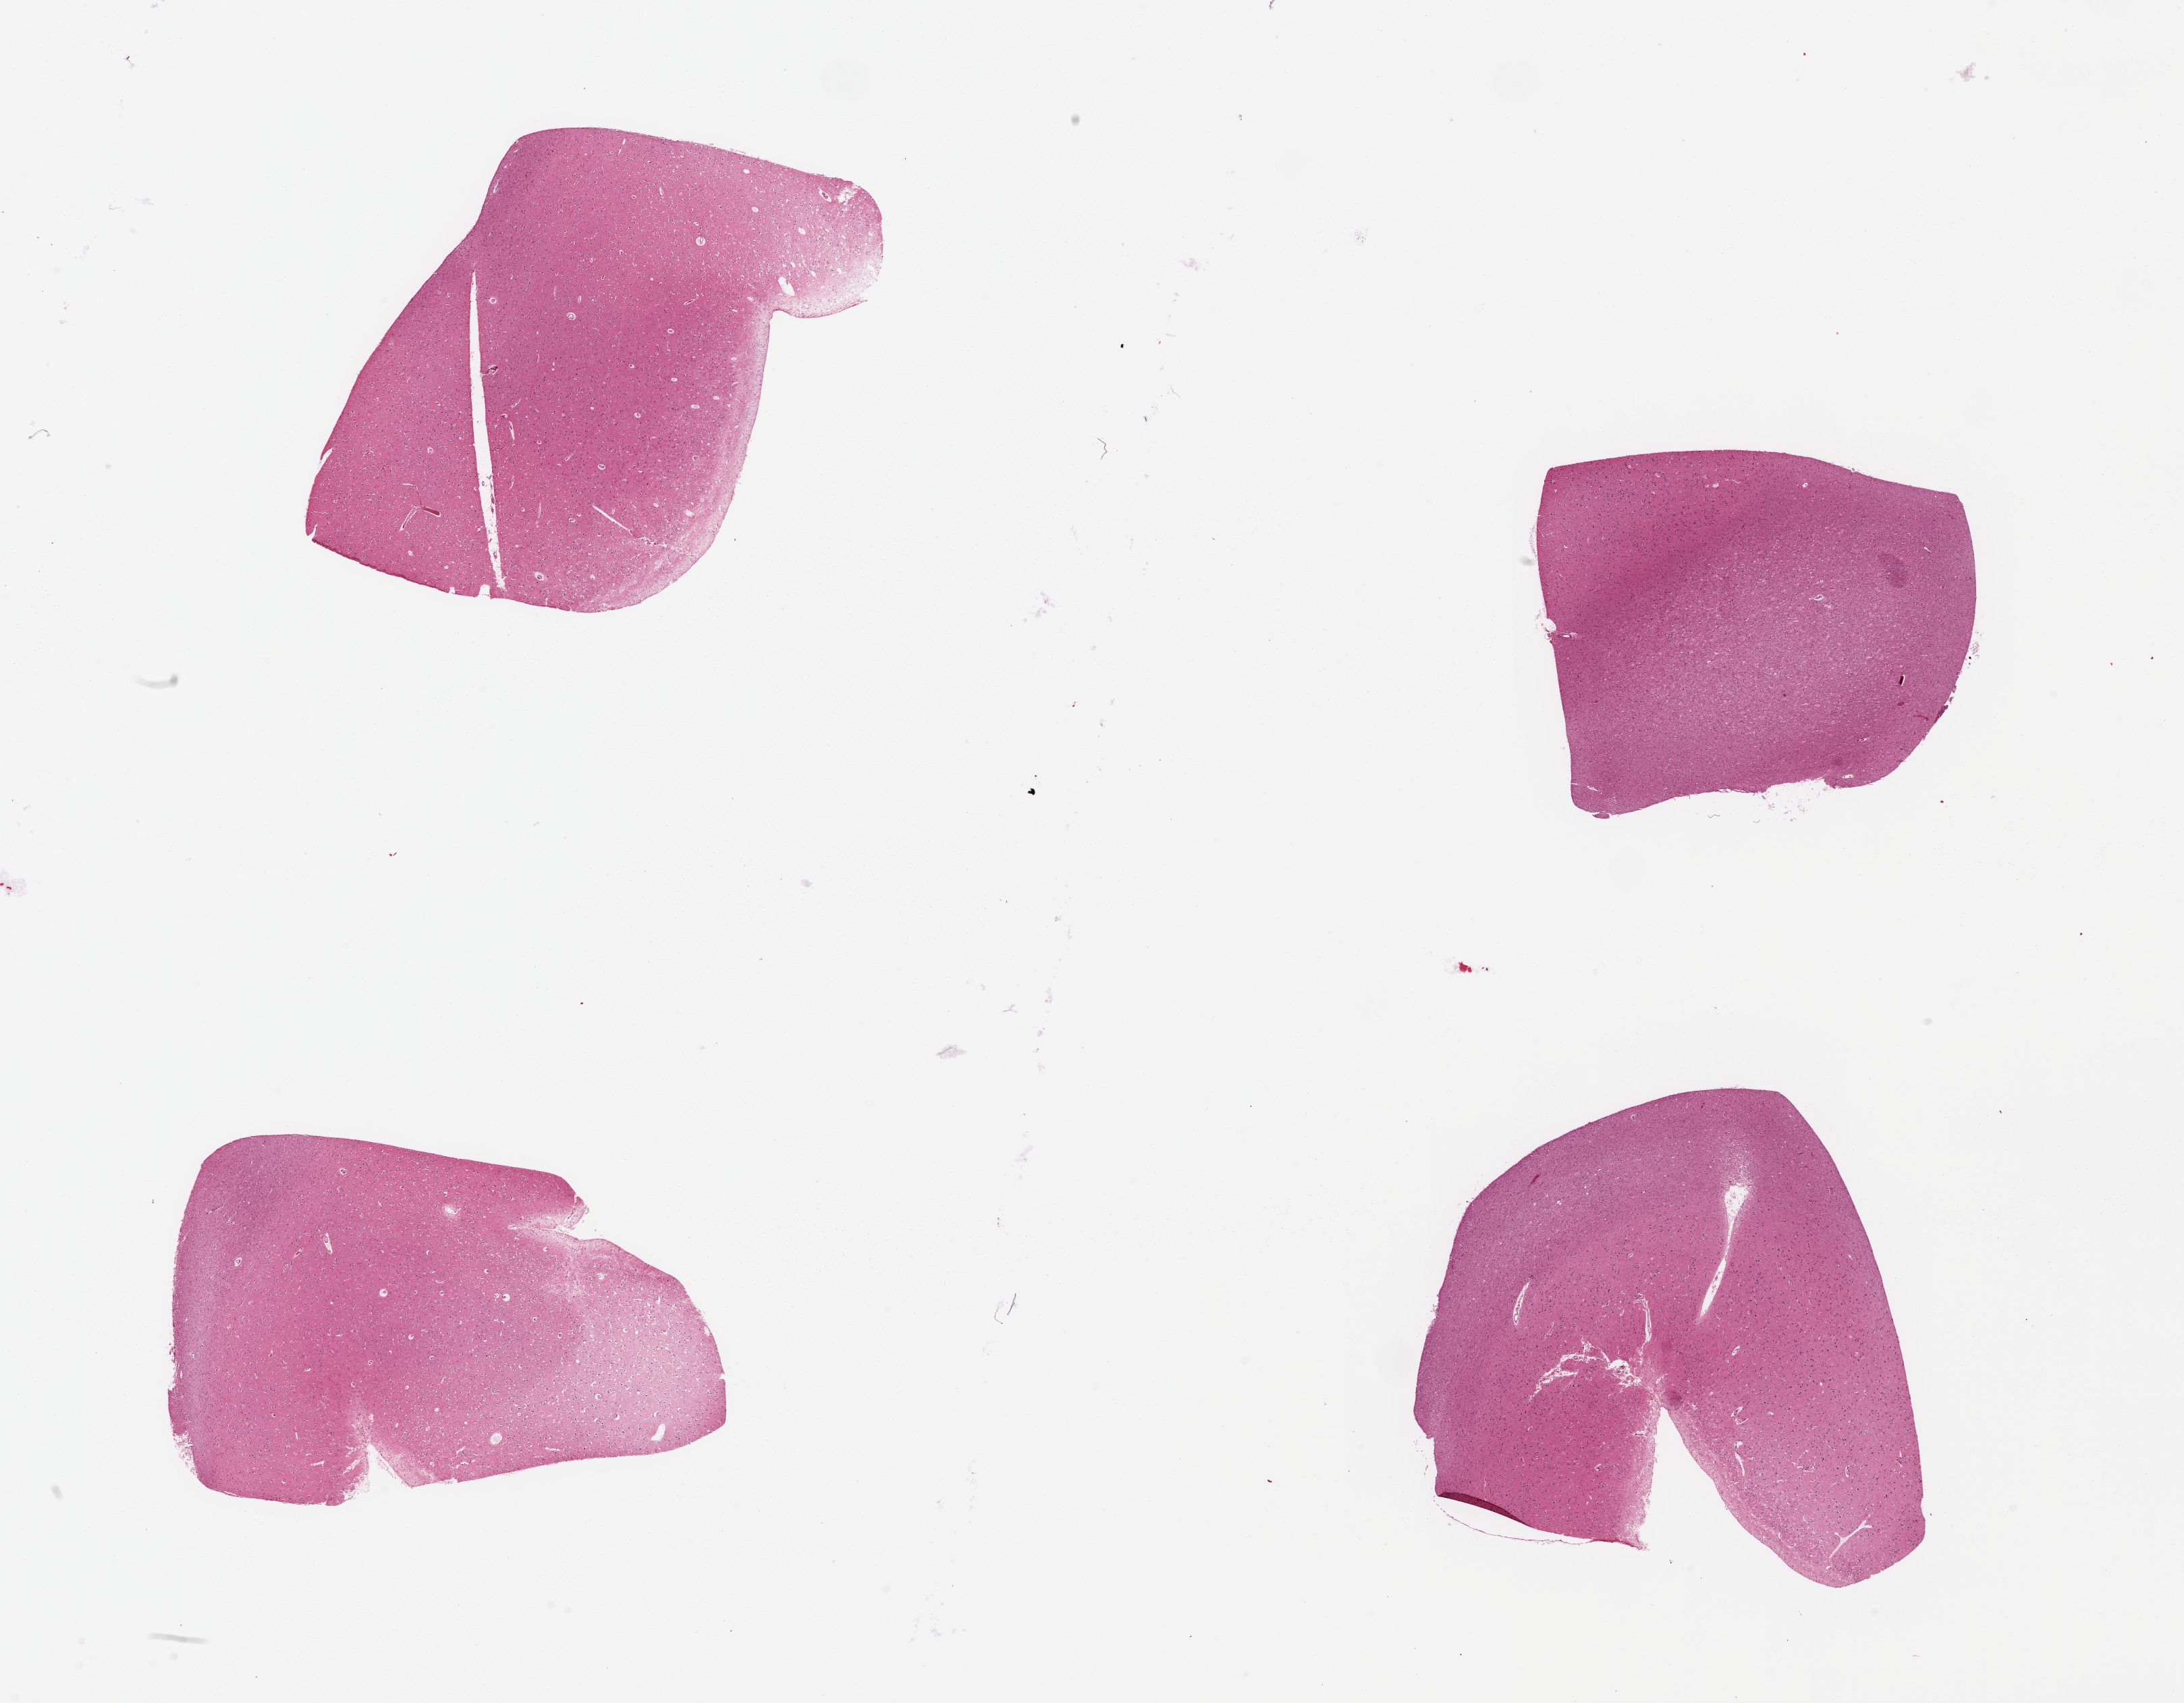
Whole-slide image, haematoxylin and eosin stain — a low-resolution overview of the entire scanned area, about 25.6 x 20.0 mm (acquisition: 20x scan). PAXgene-fixed paraffin-embedded (PFPE) section. Target tissue: cerebral cortex. Tissue donor sample. Male donor.
Reviewer comment on this tissue sample: 4 pieces, no abnormalities.